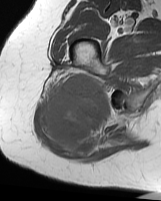
MRI of an extremity soft-tissue mass, one axial slice; slice 41 of 70 in the series (ordered by position); MR volume resampled by the dataset authors to the PET/CT grid (not the native acquisition matrix); 161 × 201 image matrix. Female patient. From the clinical record (not read from this slice): histological type: synovial sarcoma; grade: intermediate; site of the primary tumour: right buttock.
Structures marked on this image (expert contour drawn on MRI and transferred to this co-registered scan by the dataset authors):
- gross tumour volume including surrounding oedema: bounding box (x1, y1, x2, y2) in pixels: (44, 72, 111, 158)
- gross tumour volume (mass): (44, 72, 111, 148)